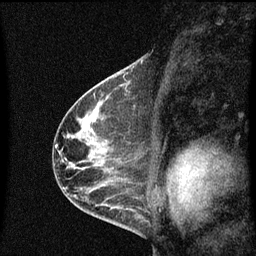
Breast MRI (dynamic contrast-enhanced), one sagittal slice; slice 40 of 60 in the series (ordered by position); dynamic contrast-enhanced series, image 2 of 3 at this slice position (ordered by acquisition); 1.5 T; TE 4.2 ms, TR 8.4 ms; 2 mm slice thickness; 256 × 256 image matrix. Female patient, age 41 years.
Structures marked on this image (semi-automatic segmentation, software-assisted and operator-edited):
- analysis volume of interest (the breast-tissue region the enhancement analysis was run in; not a lesion): bounding box (x1, y1, x2, y2) in pixels: (121, 74, 145, 99)
- tumour enhancement mask (voxels above the 70 % enhancement threshold inside the analysis volume of interest): (124, 74, 130, 93)